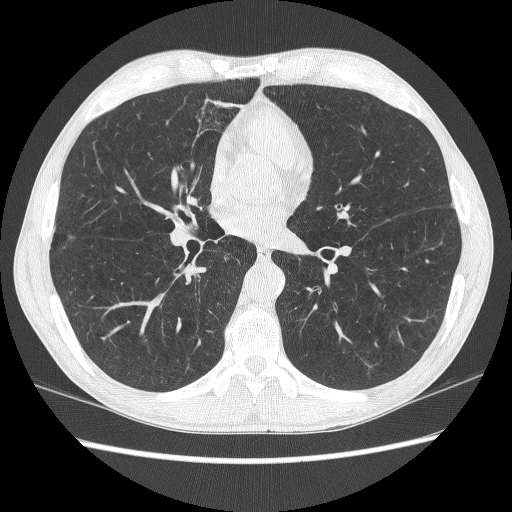
Chest CT (low-dose screening protocol), one axial image; first (baseline) screen; lung window (W 1500 / L -600 HU); slice 124 of 278 in the series. Male participant, aged 62 years at enrolment.
Lesion marked by an expert reader, bounding box (x1, y1, x2, y2) in pixels: (327, 203, 362, 236). Screening reader's record for this exam (one nodule recorded; not confirmed to be the boxed lesion): non-calcified nodule or mass ≥4 mm, right lower lobe, 8 × 4 mm, poorly defined margins, soft tissue attenuation, pre-existing on the prior screen: no. Note: the box lies in the patient's left hemithorax on this image, whereas the reader's record names the right lung; they may be different findings. Official screen result: positive, change unspecified: nodule(s) >= 4 mm or enlarging nodule(s), mass(es), or other non-specific abnormalities suspicious for lung cancer.